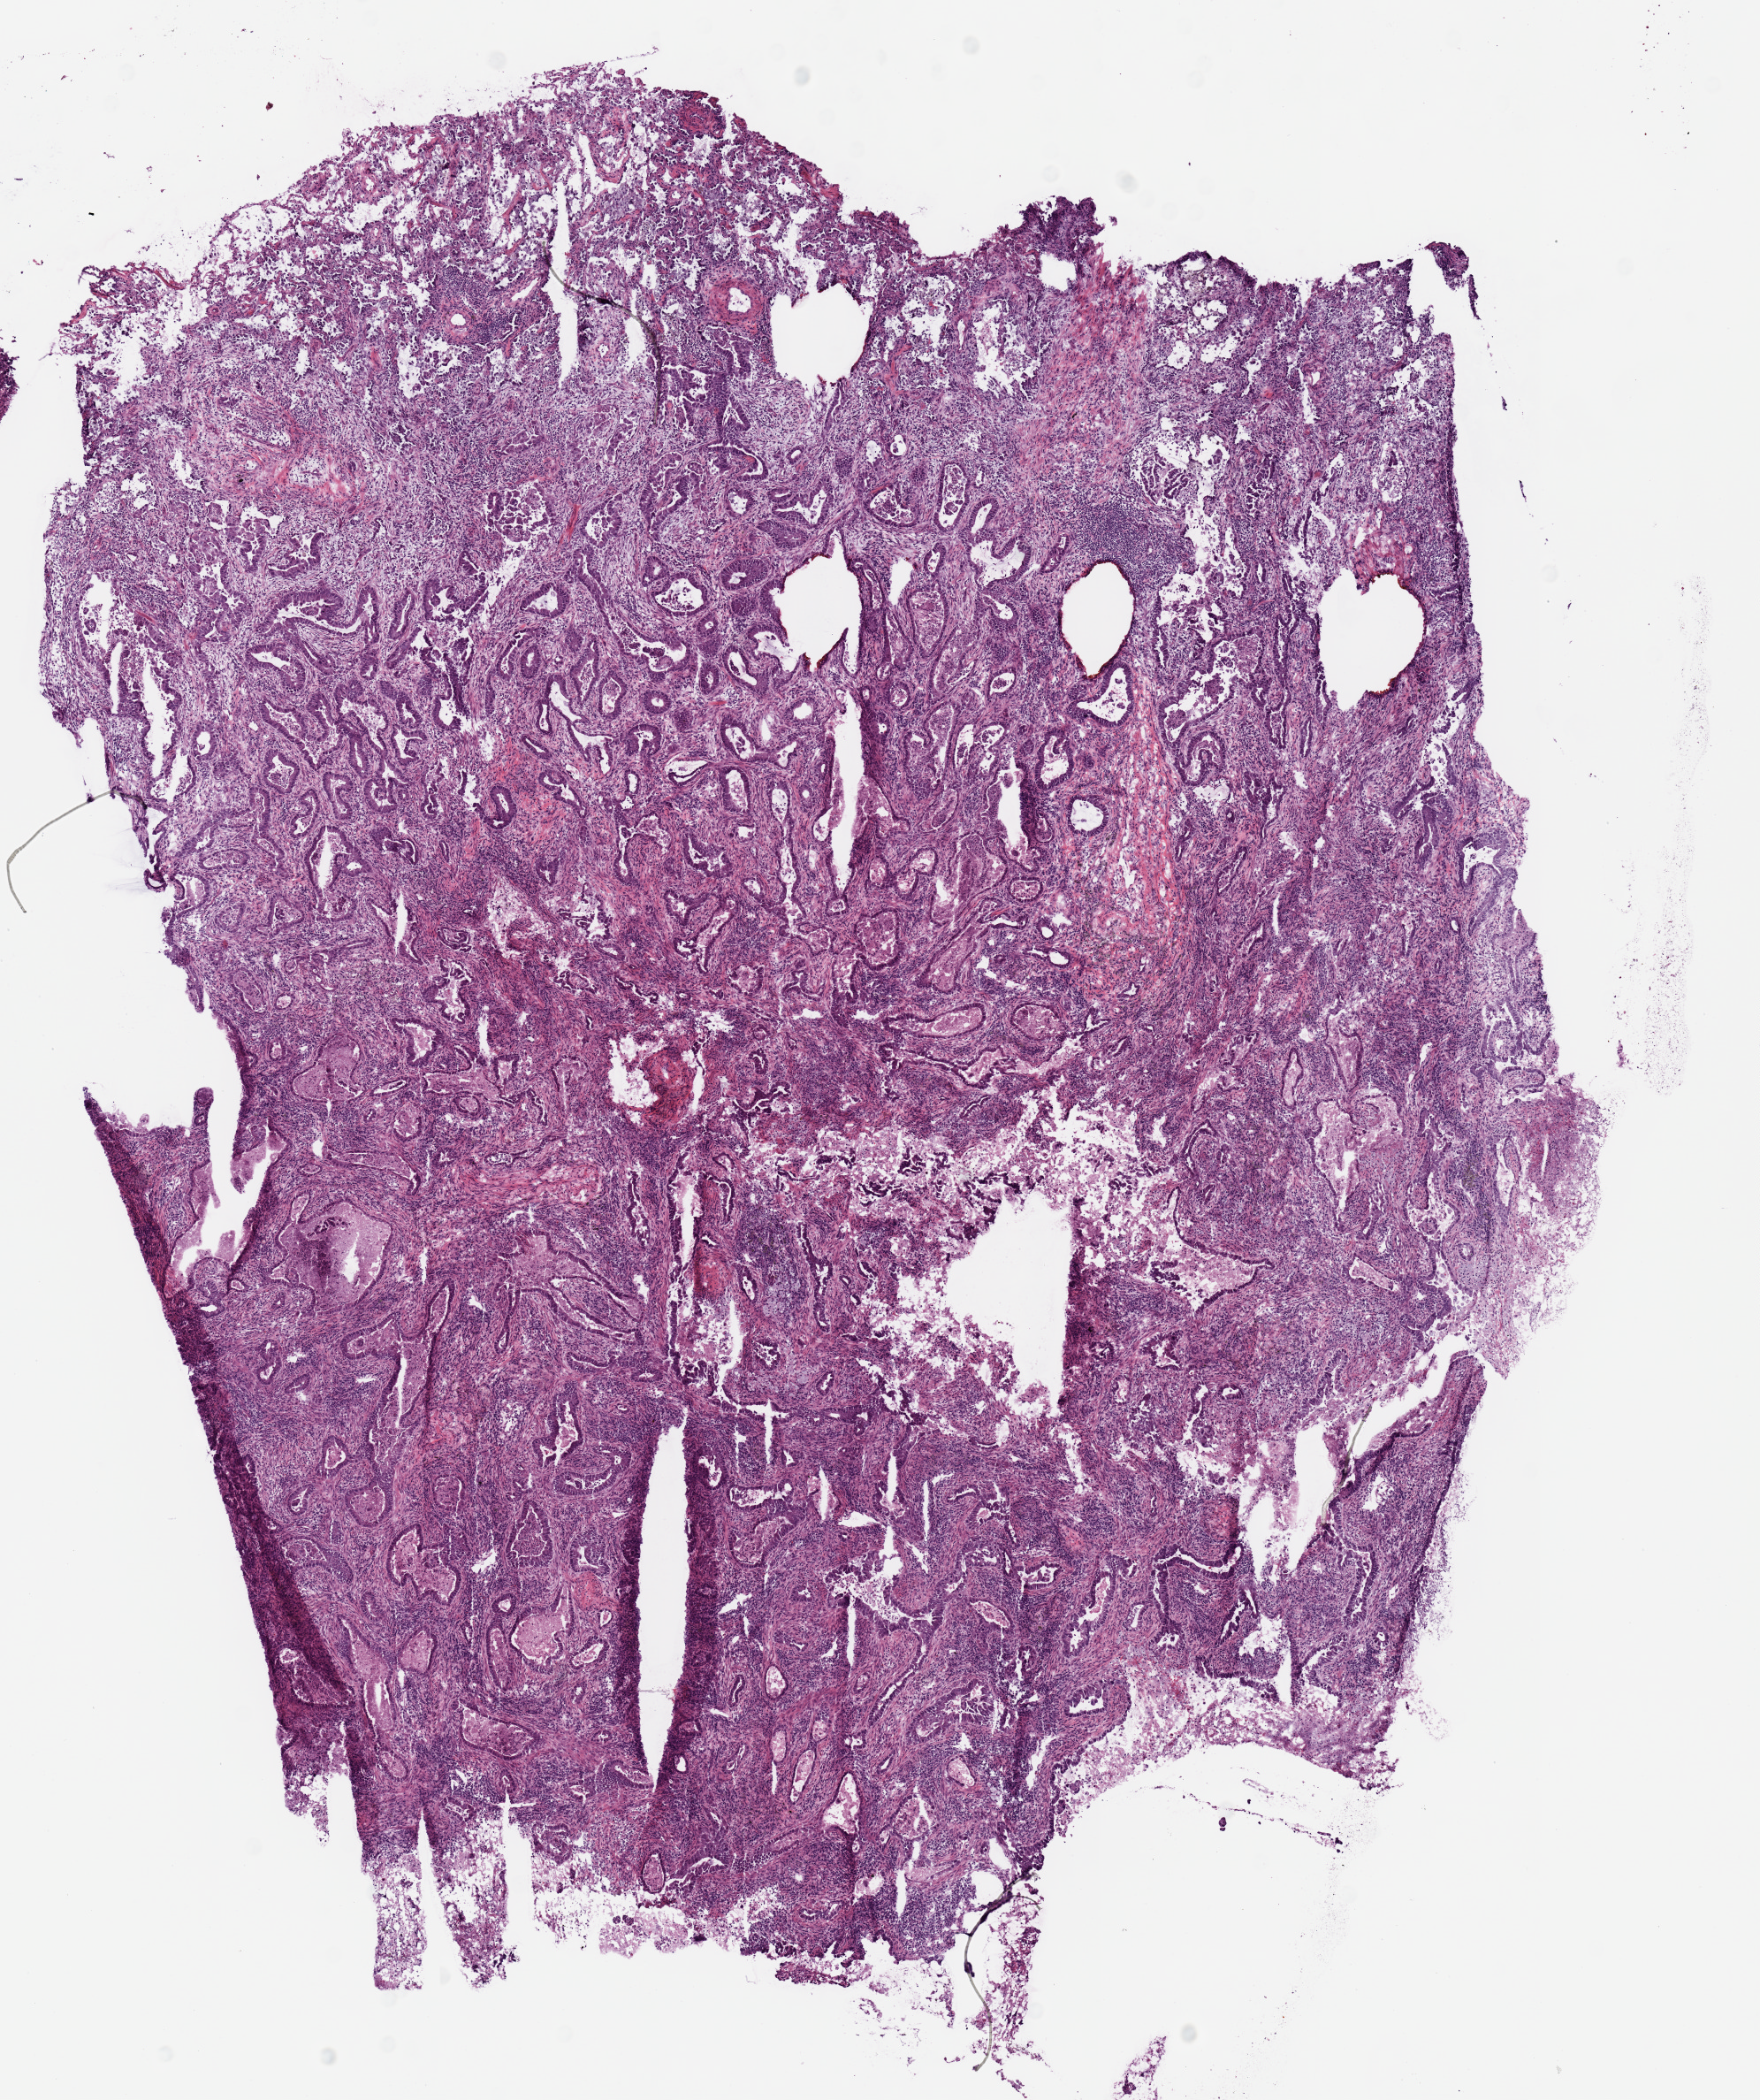
Digitized Hematoxylin and eosin (H&E) stained tissue section (whole slide) — whole scanned area (about 7.9 x 9.4 mm) shown as a low-resolution overview. Frozen section from the top of the tissue portion. Primary tumour sample from the lung. Male patient; age at initial diagnosis 69 years. Slide review estimates, as recorded: tumour cells 85%, tumour nuclei 60%, normal cells 0%, stromal cells 15%, necrosis 0%. Inflammatory infiltration, as recorded: lymphocyte infiltration 0%, monocyte infiltration 0%, neutrophil infiltration 0%.
AJCC pathologic stage: IIA (7th edition). Diagnosis: Adenocarcinoma, NOS.